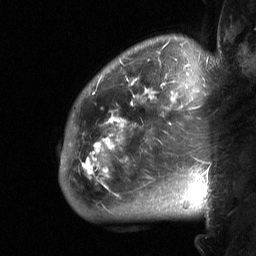
Breast MRI (dynamic contrast-enhanced), one sagittal slice; position 52 of 64 along the scan axis; dynamic contrast-enhanced study with each time point stored as its own series, time point 2 of 3 at this slice position (early post-contrast, ordered by acquisition time); 1.5 T; TE 4.8 ms, TR 27 ms; 2 mm slice thickness; 256 × 256 image matrix, field of view 200 × 200 mm. Female patient, age 50 years. Case-level facts recorded for this patient, not image findings: setting: breast cancer imaged before/during neoadjuvant chemotherapy; receptor status: HER2-positive.
Outlined on this slice (semi-automatic segmentation, software-assisted and operator-edited):
- analysis volume of interest (the breast-tissue region the enhancement analysis was run in; not a lesion): bounding box [x1, y1, x2, y2] px = [60, 62, 220, 222]
- tumour enhancement mask (voxels above the 90 % enhancement threshold inside the analysis volume of interest): [81, 78, 208, 191]